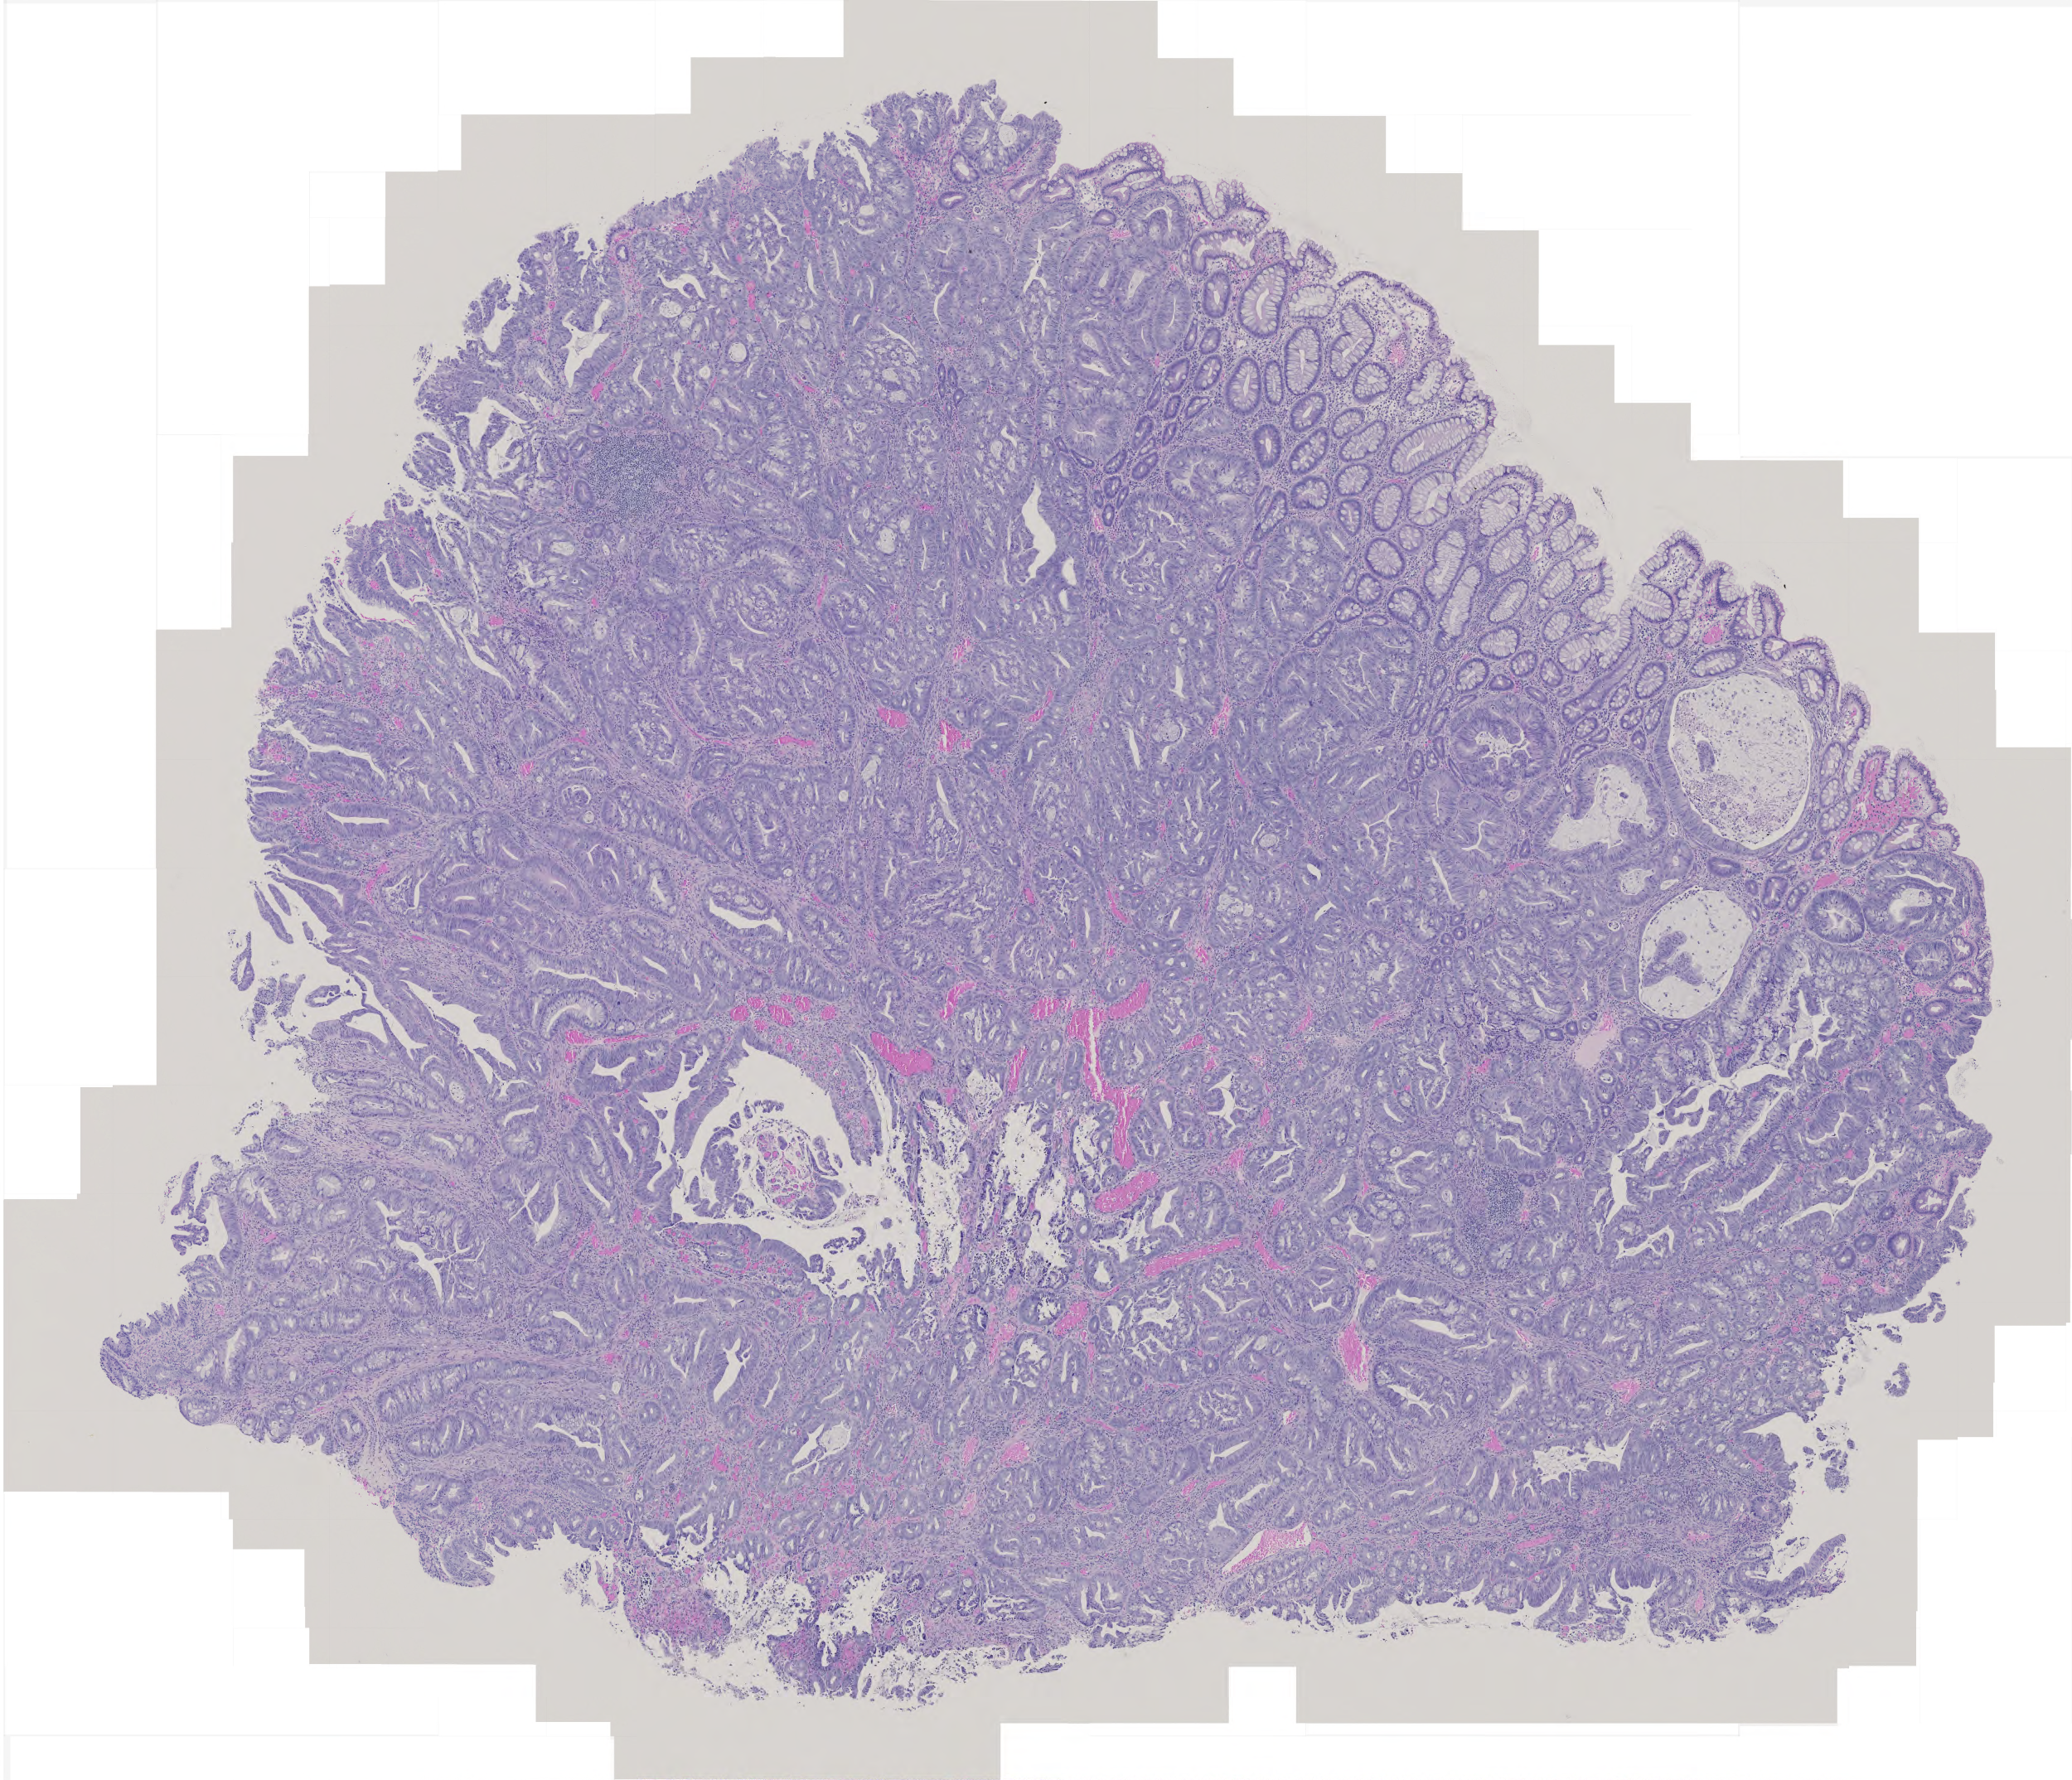
H&E whole-slide image, shown as a low-resolution overview of the whole scanned area (about 5.0 x 4.3 mm); formalin-fixed paraffin-embedded (FFPE) diagnostic section; sample: primary tumour, colon. Male patient; age at initial diagnosis 68 years.
Diagnosis: Adenocarcinoma, NOS (sigmoid colon). AJCC pathologic stage: II. TNM: T3 N0 M0.